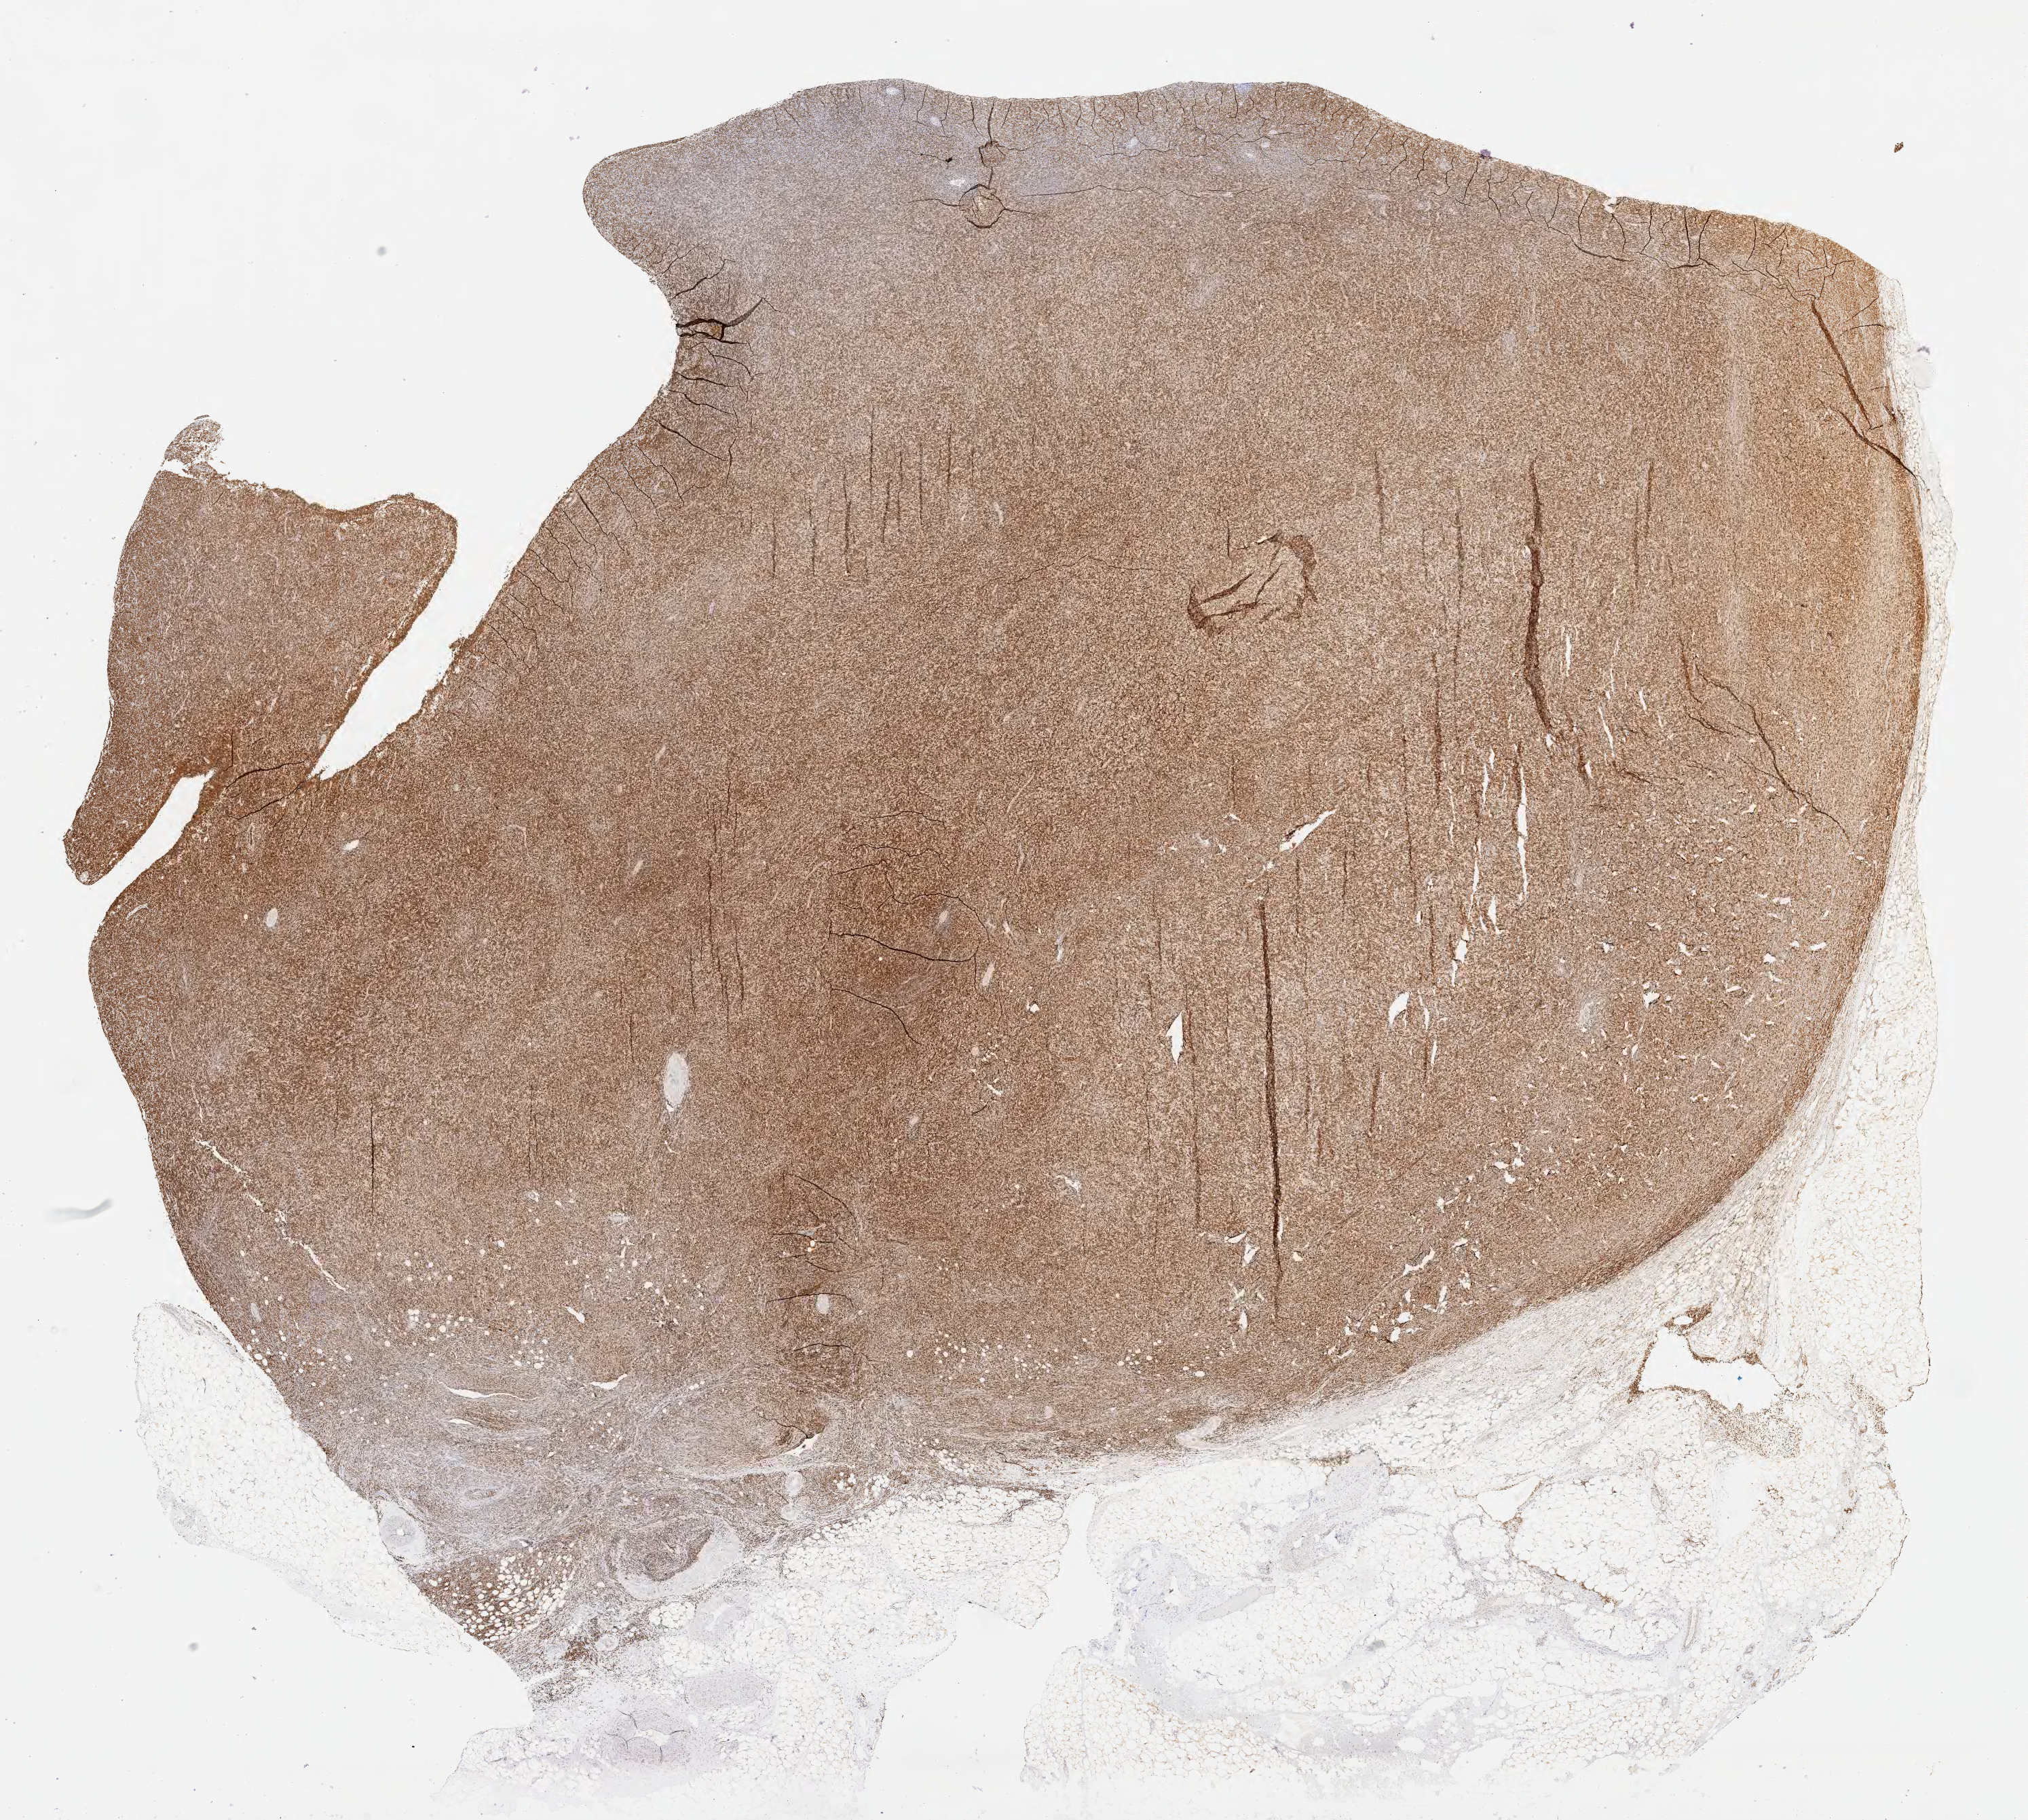
Immunohistochemistry (IHC) whole-slide image stained for BCL2, shown as a low-resolution overview of the whole scanned area (about 24.1 x 21.7 mm), specimen: tumor tissue, anatomic site: lymph node. Patient male; age 54 years.
• histologic diagnosis: Diffuse large B-cell lymphoma, NOS